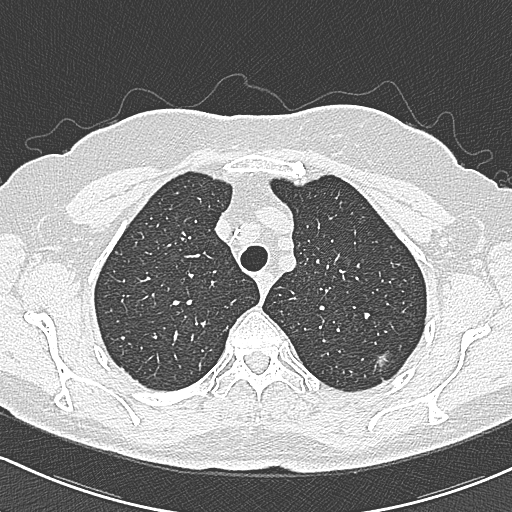
Low-dose screening chest CT, axial slice; first (baseline) screen; lung window (W 1500 / L -600 HU); 1 mm slice thickness; lung (sharp) reconstruction kernel (B80f); slice 57 of 312 in the series. Female participant, aged 65 years at enrolment. Current smoker at enrolment.
Lesion marked by an expert reader, bounding box <368,344,404,381> (left, top, right, bottom; pixels). The screening reader recorded 3 non-calcified nodules or masses ≥4 mm on this exam; which of them this box marks is not recorded. Lung cancer was diagnosed 390 days after this screen (after the second annual screen): bronchiolo-alveolar carcinoma, non-mucinous, left upper lobe, stage IA (AJCC 6th edition), 10 mm at pathology.